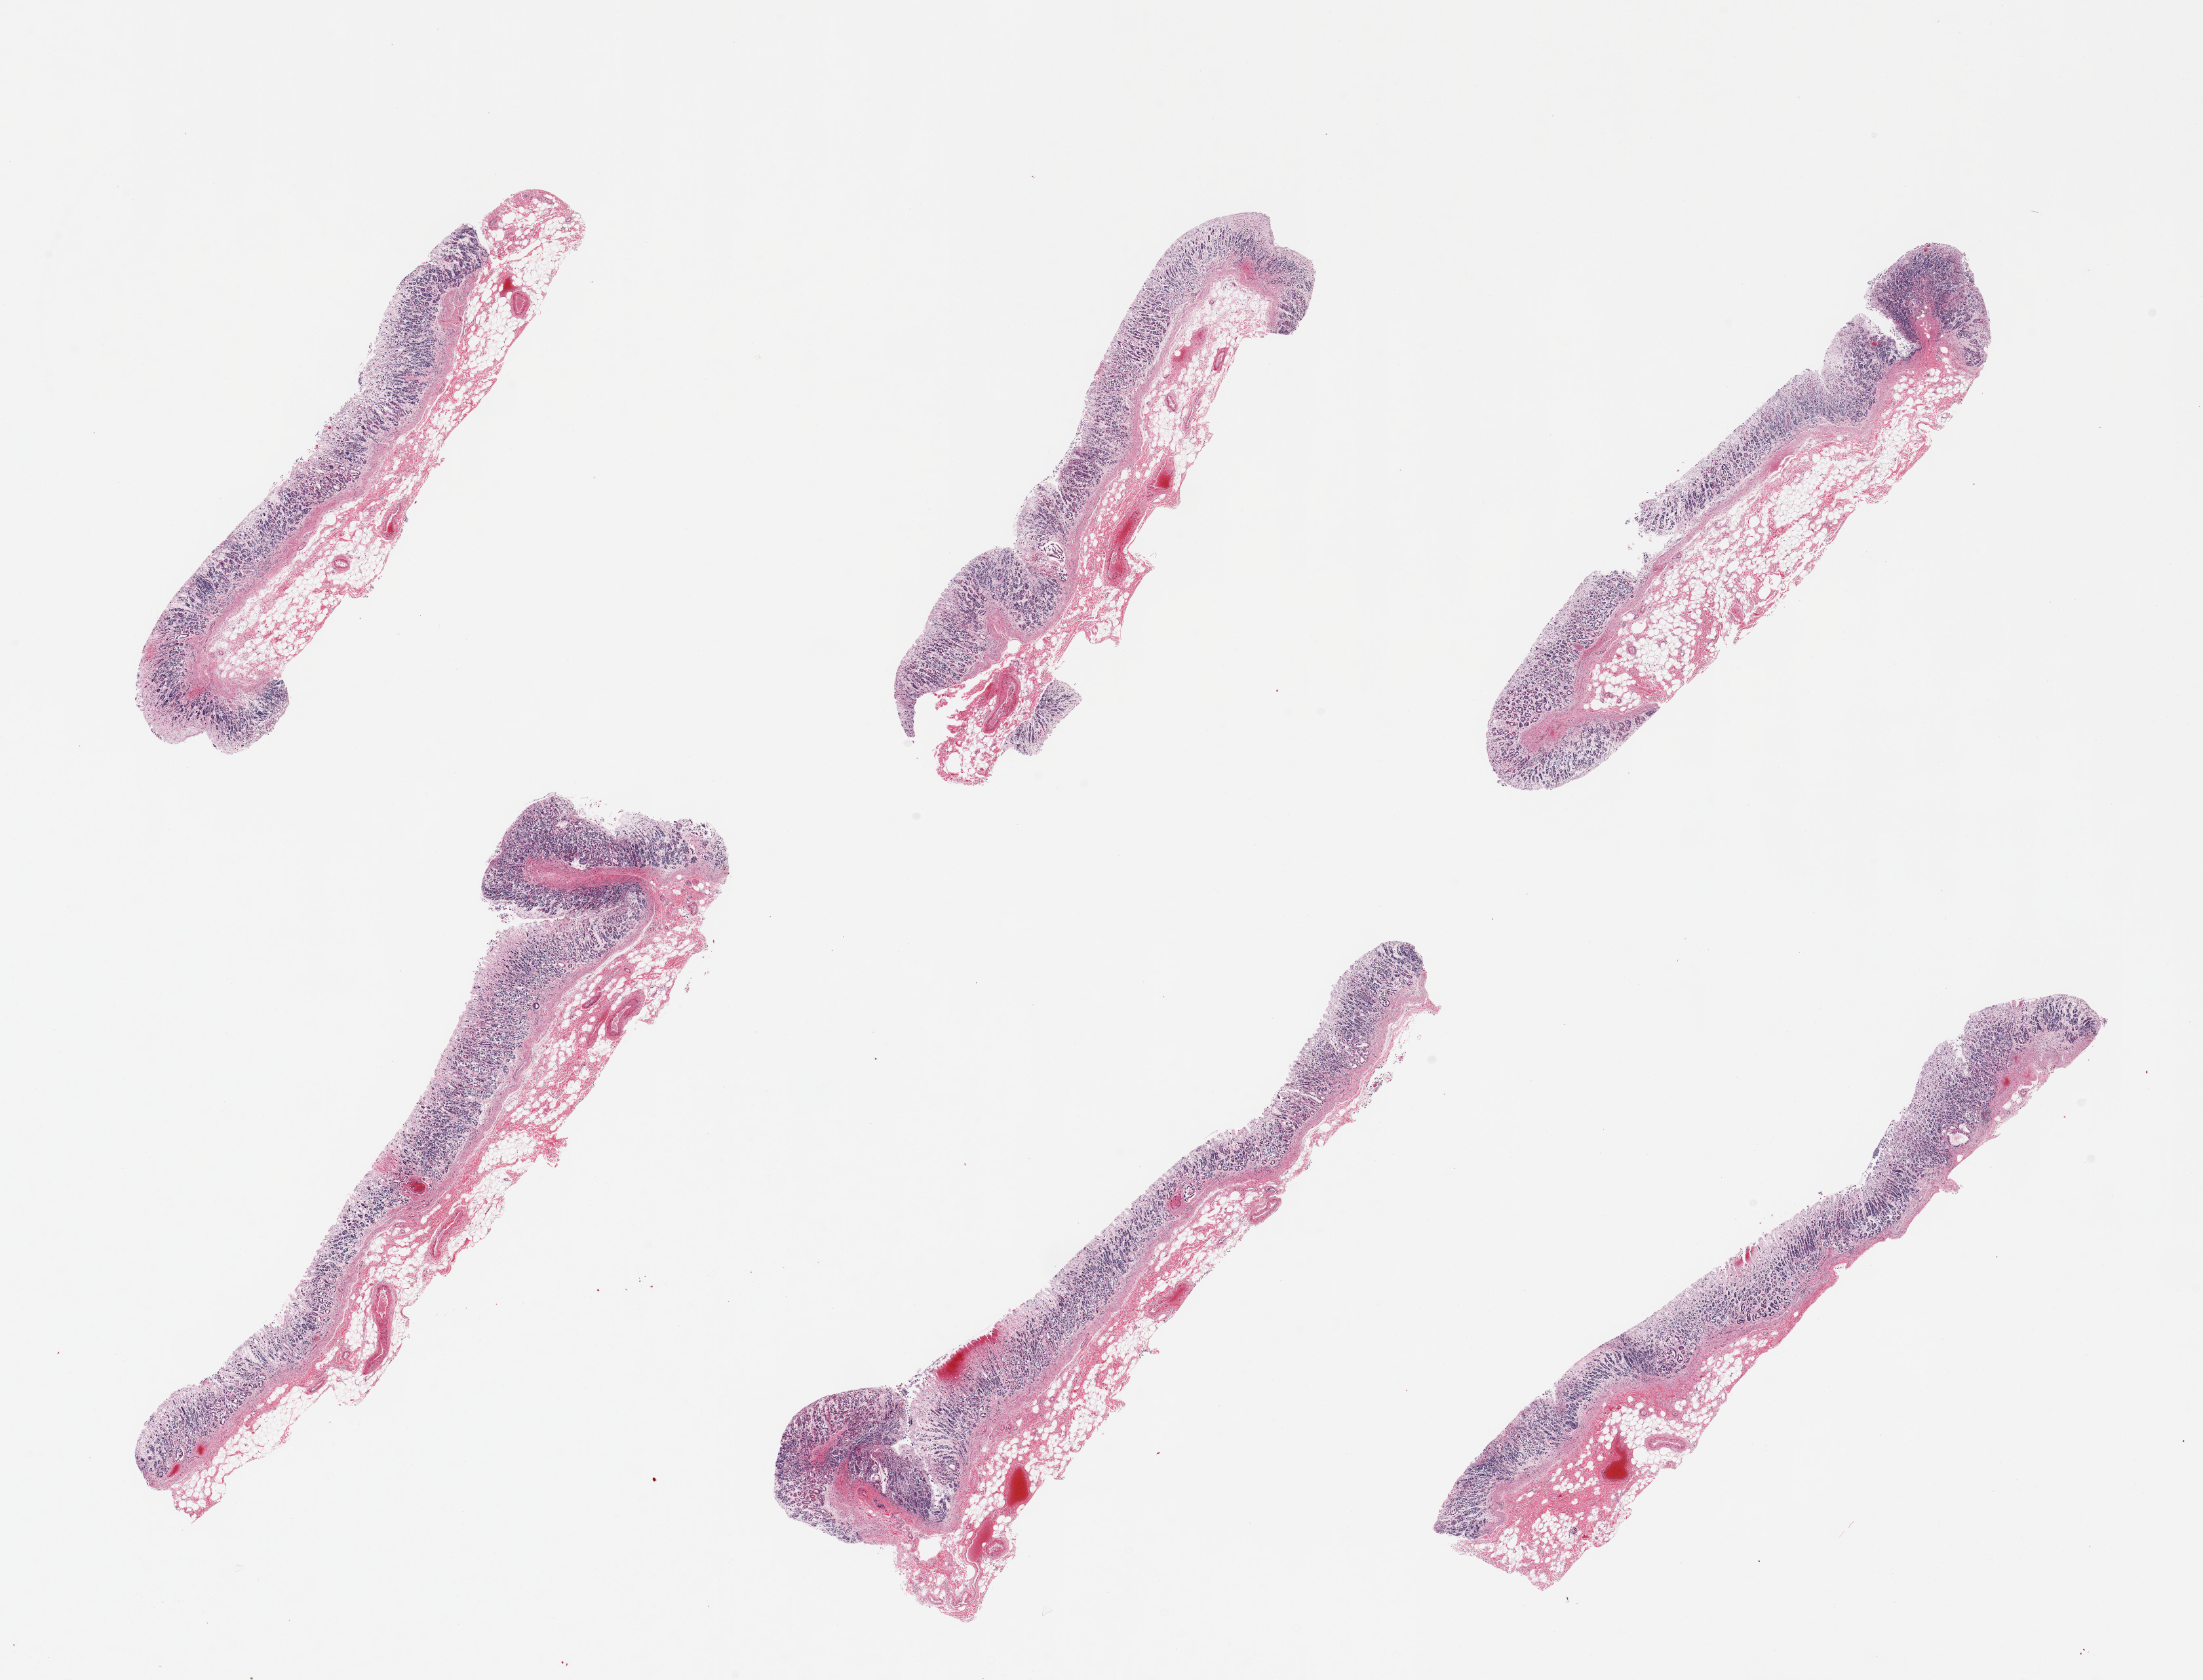
Whole-slide image, H&E stain — a low-resolution overview of the entire scanned area, about 26.6 x 20.3 mm (acquisition: 20x scan); PAXgene-fixed paraffin-embedded (PFPE) section; section of stomach (target tissue); donor tissue sample. Donor: male.
Pathologist's review note for this sample: 6 pieces; mucosa only present: autolyzed.